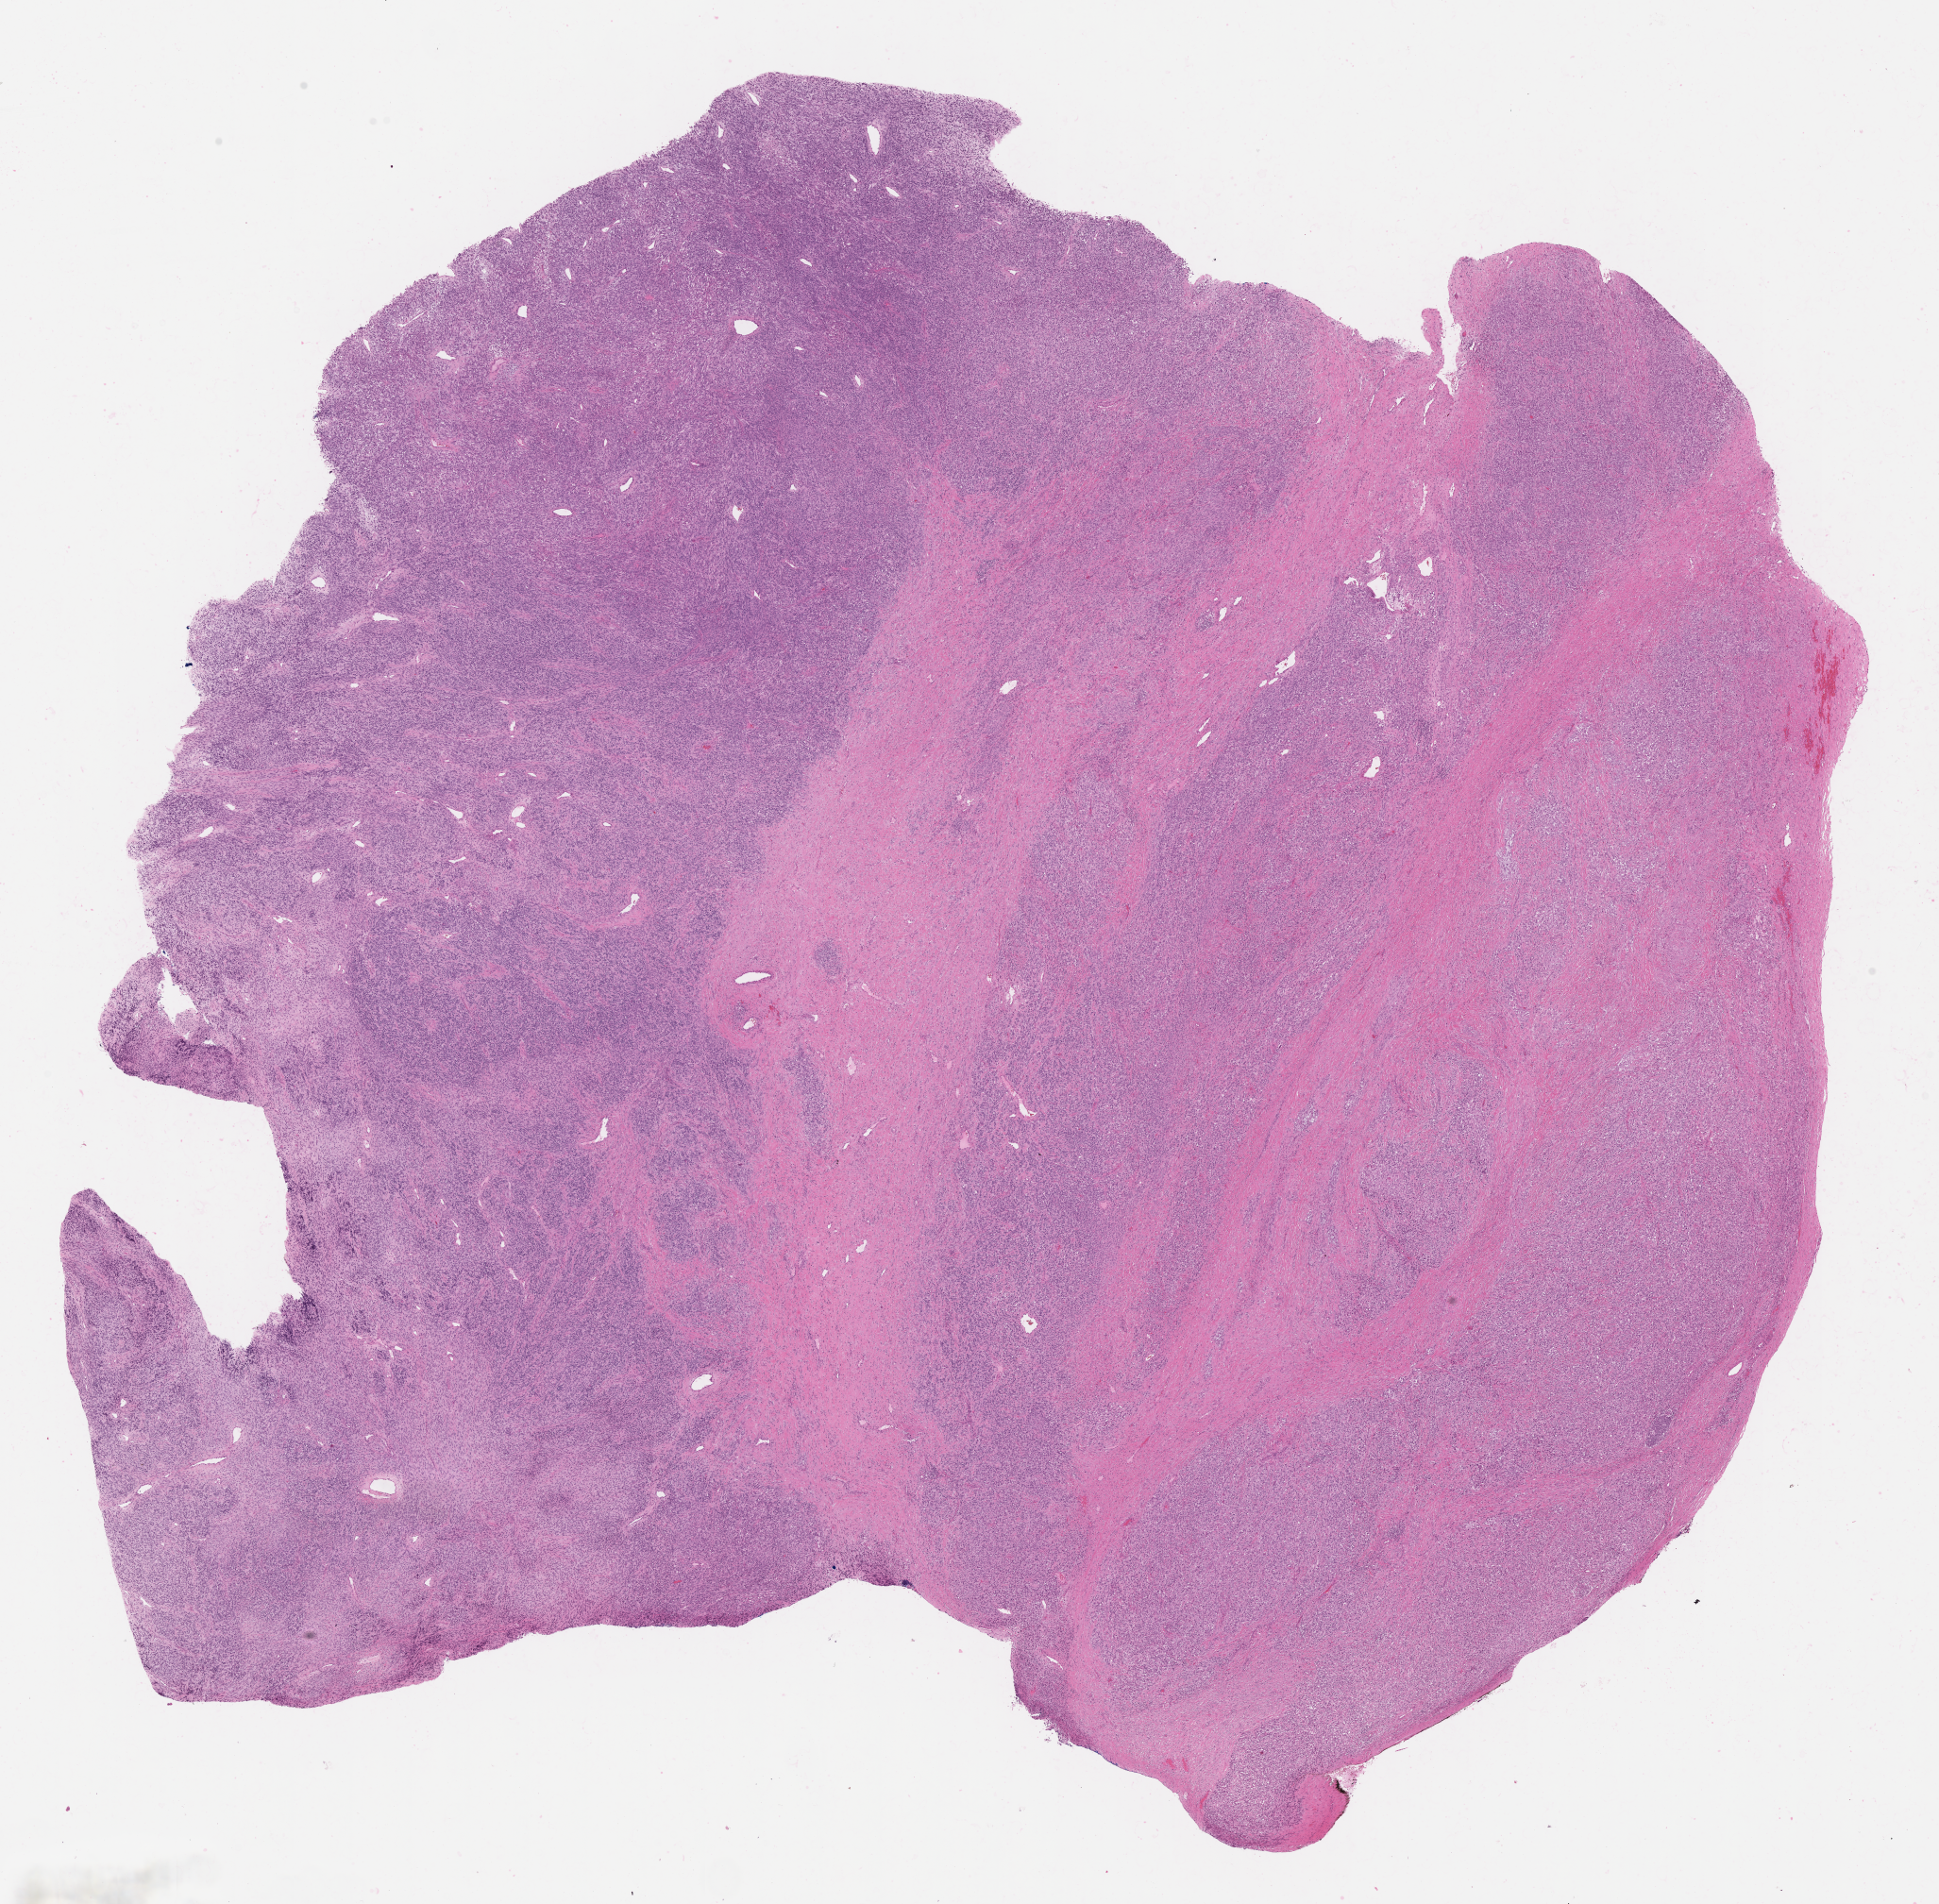
Digitized hematoxylin and eosin (H&E)-stained section of tumor tissue — shown as a low-resolution overview of the whole scanned area (about 16.6 x 16.3 mm). FFPE section. Female patient, age at diagnosis 4.2 years.
Metastatic status at presentation (as recorded): non-metastatic. Diagnosis: rhabdomyosarcoma; histological classification: spindle cell rhabdomyosarcoma. Stage (as recorded): 3.